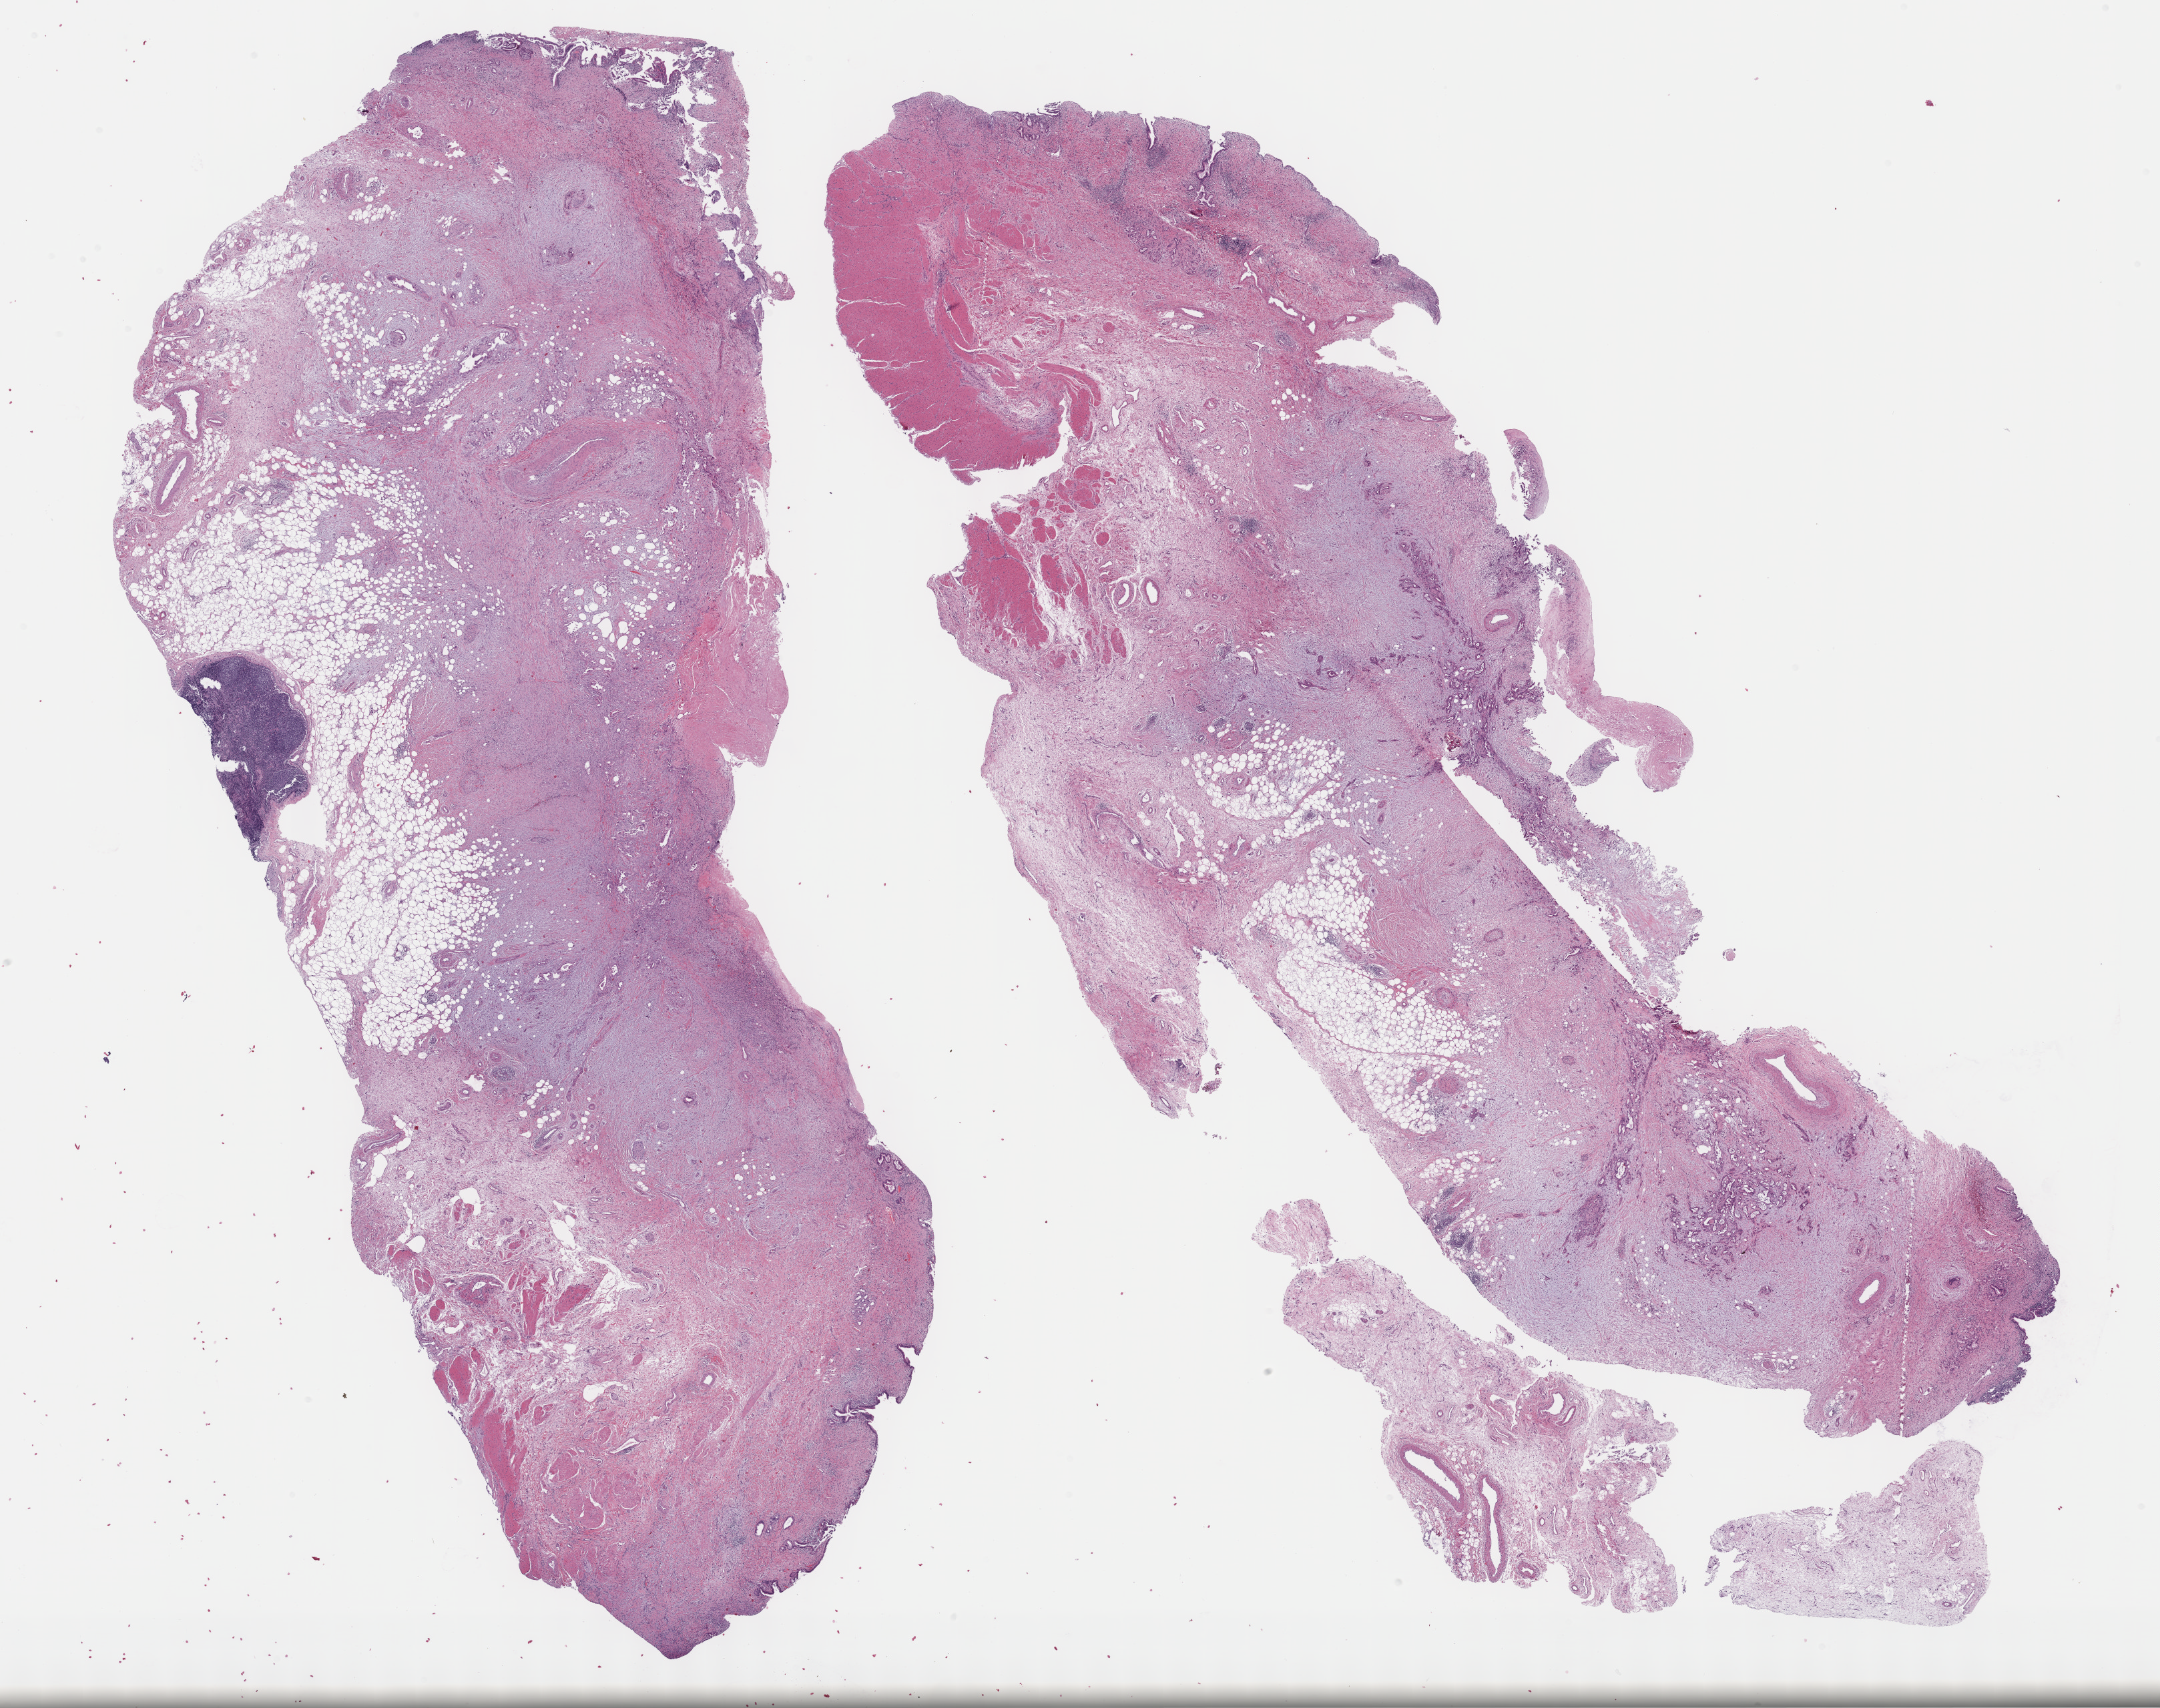
Whole-slide histology image, H&E, a low-resolution overview of the entire scanned area, about 26.2 x 20.7 mm (from a 40x scan); formalin-fixed paraffin-embedded (FFPE) diagnostic section; sample: primary tumour, bile duct. Patient: female, age at initial diagnosis 70 years. Histologic grade: G3 (poorly differentiated).
Pathologic diagnosis: Cholangiocarcinoma. AJCC pathologic stage: III (7th edition).